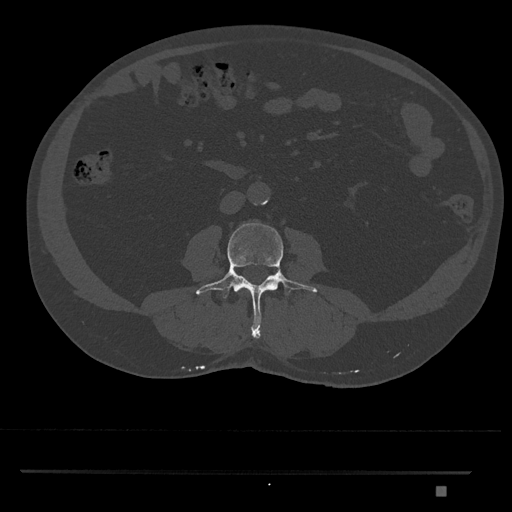
CT including the spine, one axial slice. Position 681 of 1134 along the scan axis. Reconstruction kernel Br40s/3. Bone window (W 1800 / L 400 HU). 0.5 mm slice thickness. 512 × 512 image matrix, field of view 429 × 429 mm. Male patient, age 65 years. From the clinical record (not read from this slice): primary cancer: prostate.
Annotated regions visible in this slice (semi-automatic segmentation, software-assisted and operator-edited):
- L3 vertebra: bounding box (x1, y1, x2, y2) in pixels: (196, 222, 317, 339)